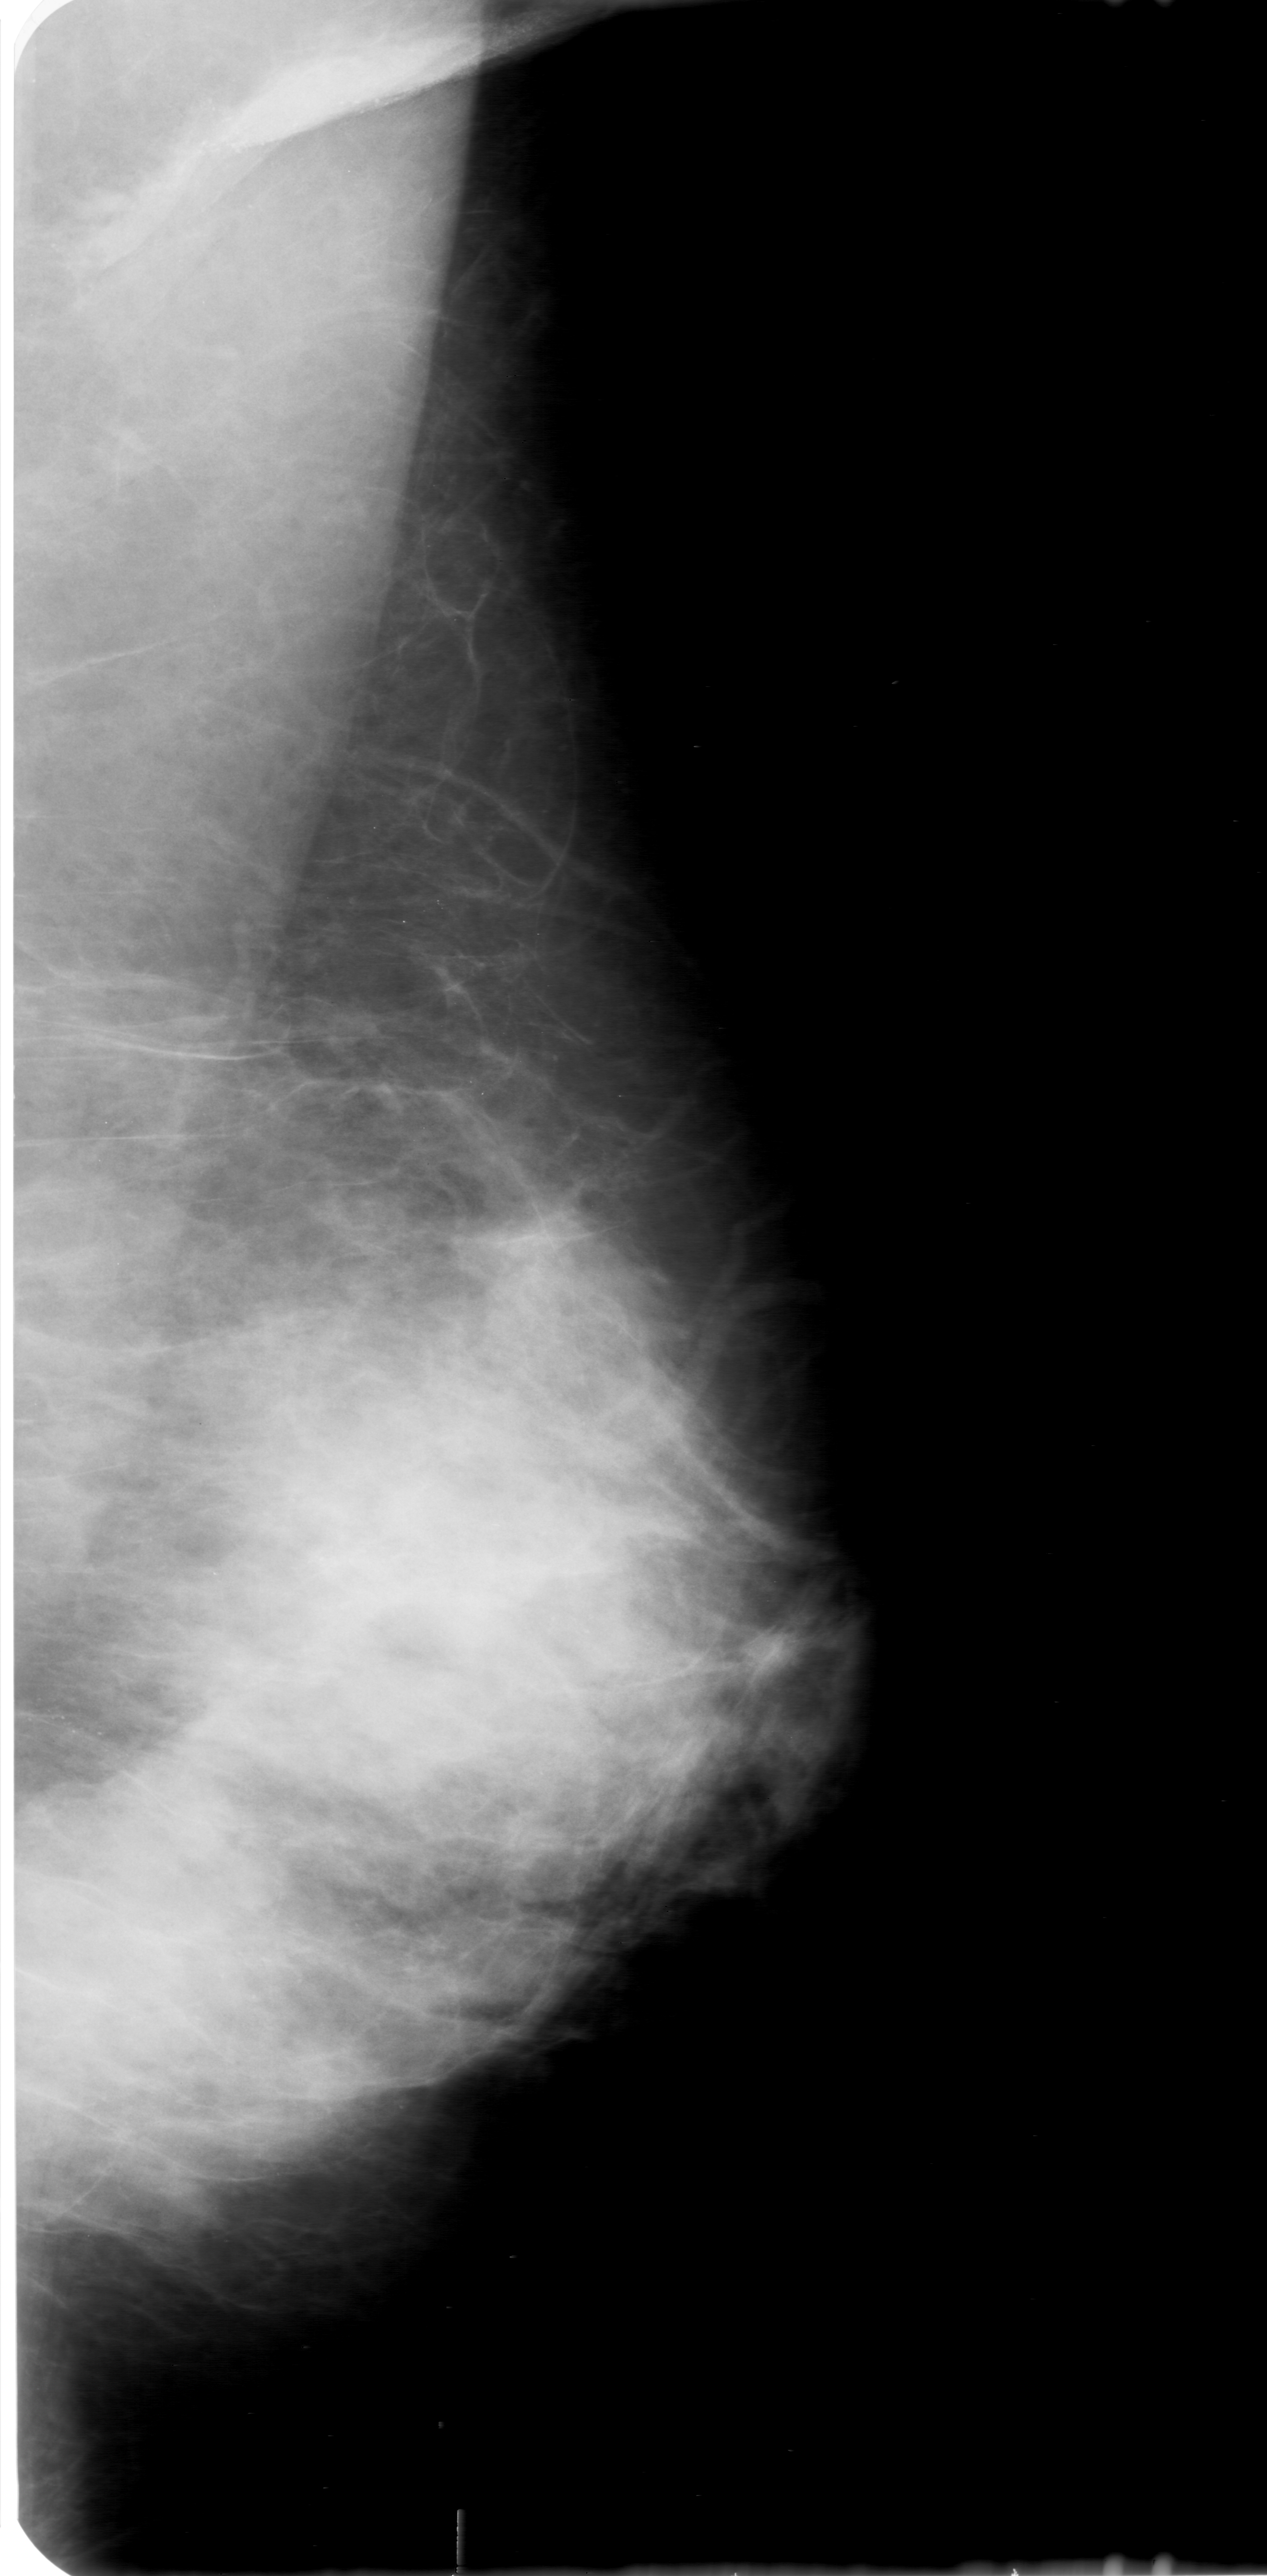
Digitized screen-film mammogram; left breast; mediolateral oblique (MLO) view; breast composition: extremely dense (BI-RADS density category 4 of 4).
Marked findings (only marked abnormalities are described; nothing is implied about the rest of the image): calcifications, morphology pleomorphic, distribution clustered; BI-RADS assessment category 0 (incomplete: needs additional imaging); pathology result (as recorded, not read from the image): malignant.